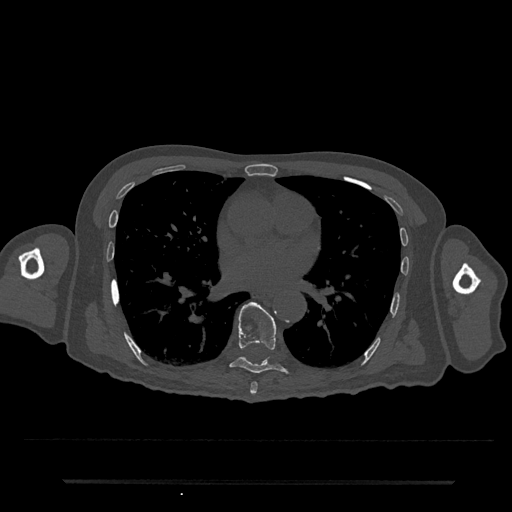
CT including the spine, one axial slice. Reconstruction kernel Br40s/3. Bone window (W 1800 / L 400 HU). 512 × 512 image matrix, field of view 427 × 427 mm. Patient: male, 74 years. Case-level facts recorded for this patient, not image findings: primary cancer: prostate.
Outlined on this slice (semi-automatic segmentation, software-assisted and operator-edited):
- T7 vertebra: bounding box <250,382,258,395> (left, top, right, bottom; pixels)
- T8 vertebra: <230,302,288,373>